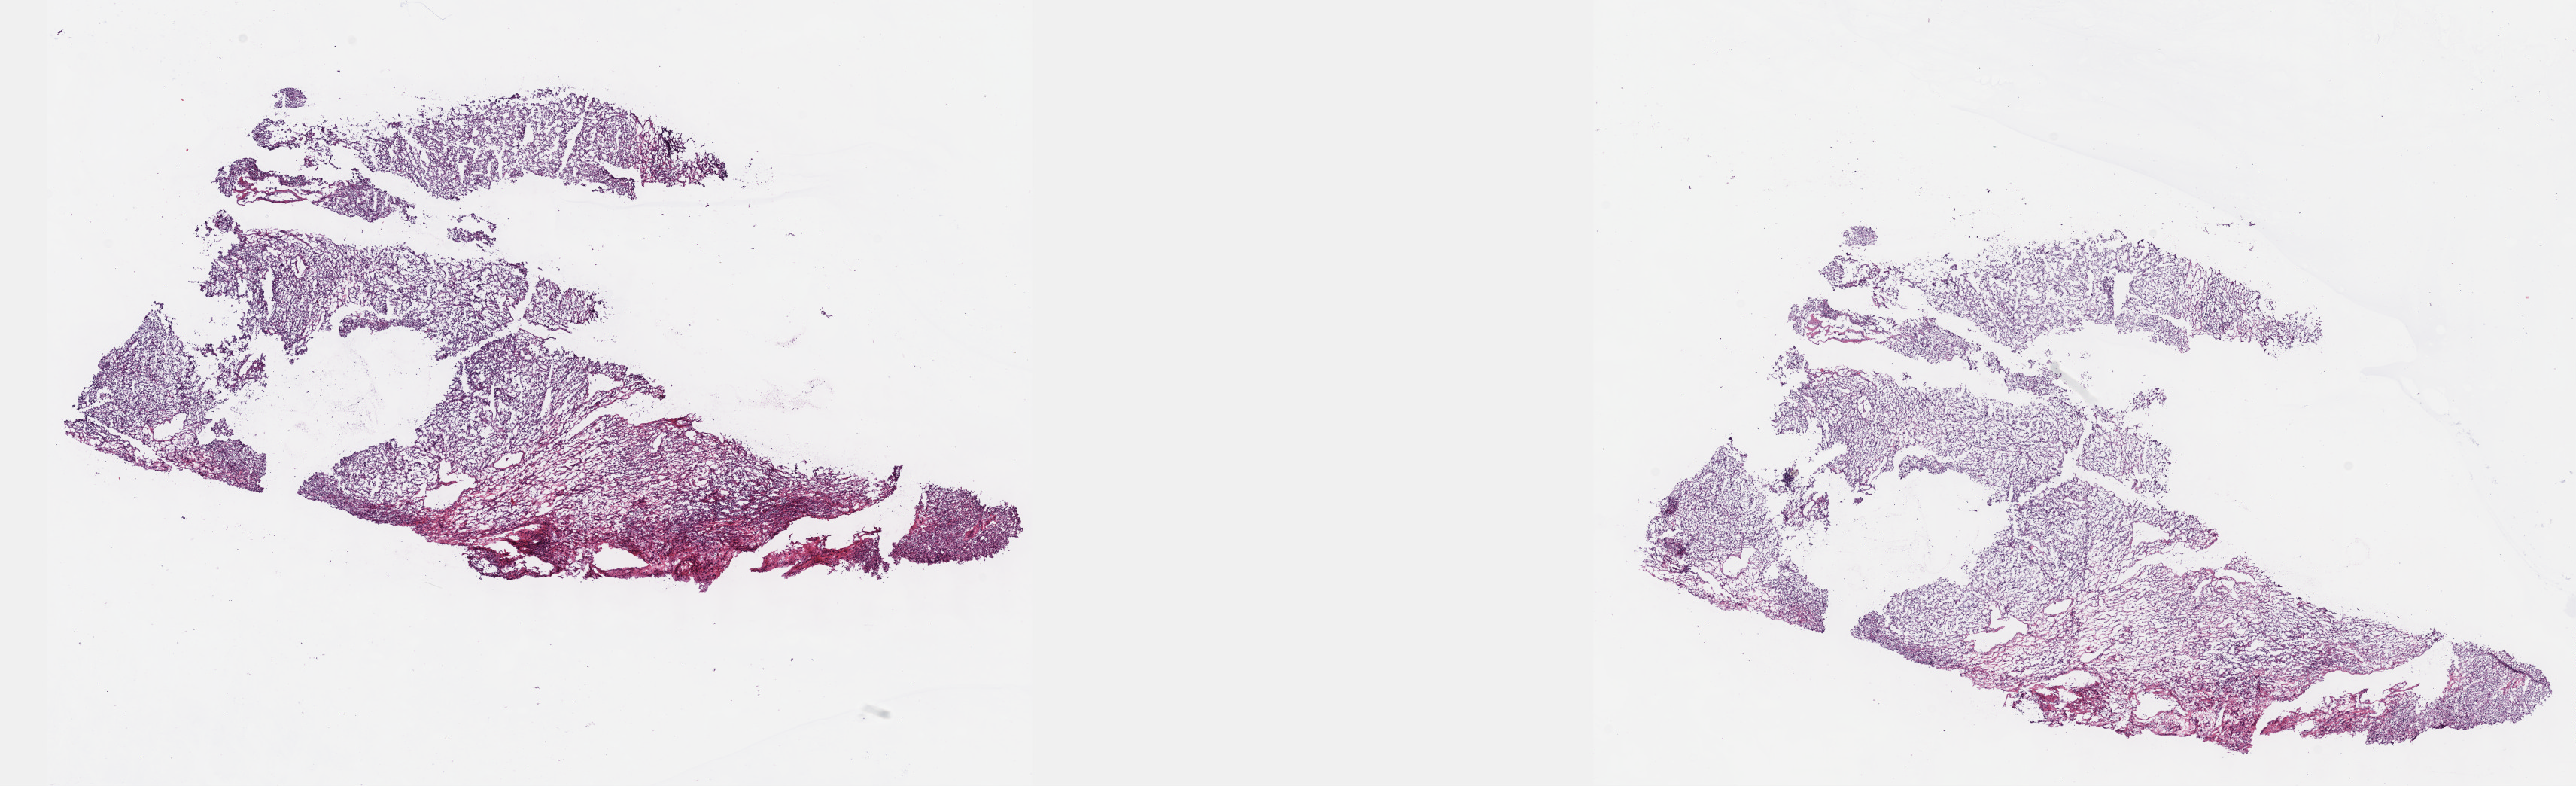
Digitized Hematoxylin and eosin (H&E) stained tissue section (whole slide), whole scanned area (about 27.7 x 8.4 mm, slide scanned at 40x) shown as a low-resolution overview. Frozen section from the top of the tissue portion. Sample: primary tumour, kidney. Patient: male, age at initial diagnosis 55 years. Histologic grade: G3 (poorly differentiated). Pathologist review of this section (percent, as recorded): tumour cells 63%, tumour nuclei 90%, normal cells 0%, stromal cells 35%, necrosis 2%. Inflammatory infiltration, as recorded: lymphocyte infiltration 4%, monocyte infiltration 0%, neutrophil infiltration 0%.
• histologic diagnosis: Clear cell adenocarcinoma, NOS
• TNM: T2a NX MX
• AJCC pathologic stage: IV (7th edition)